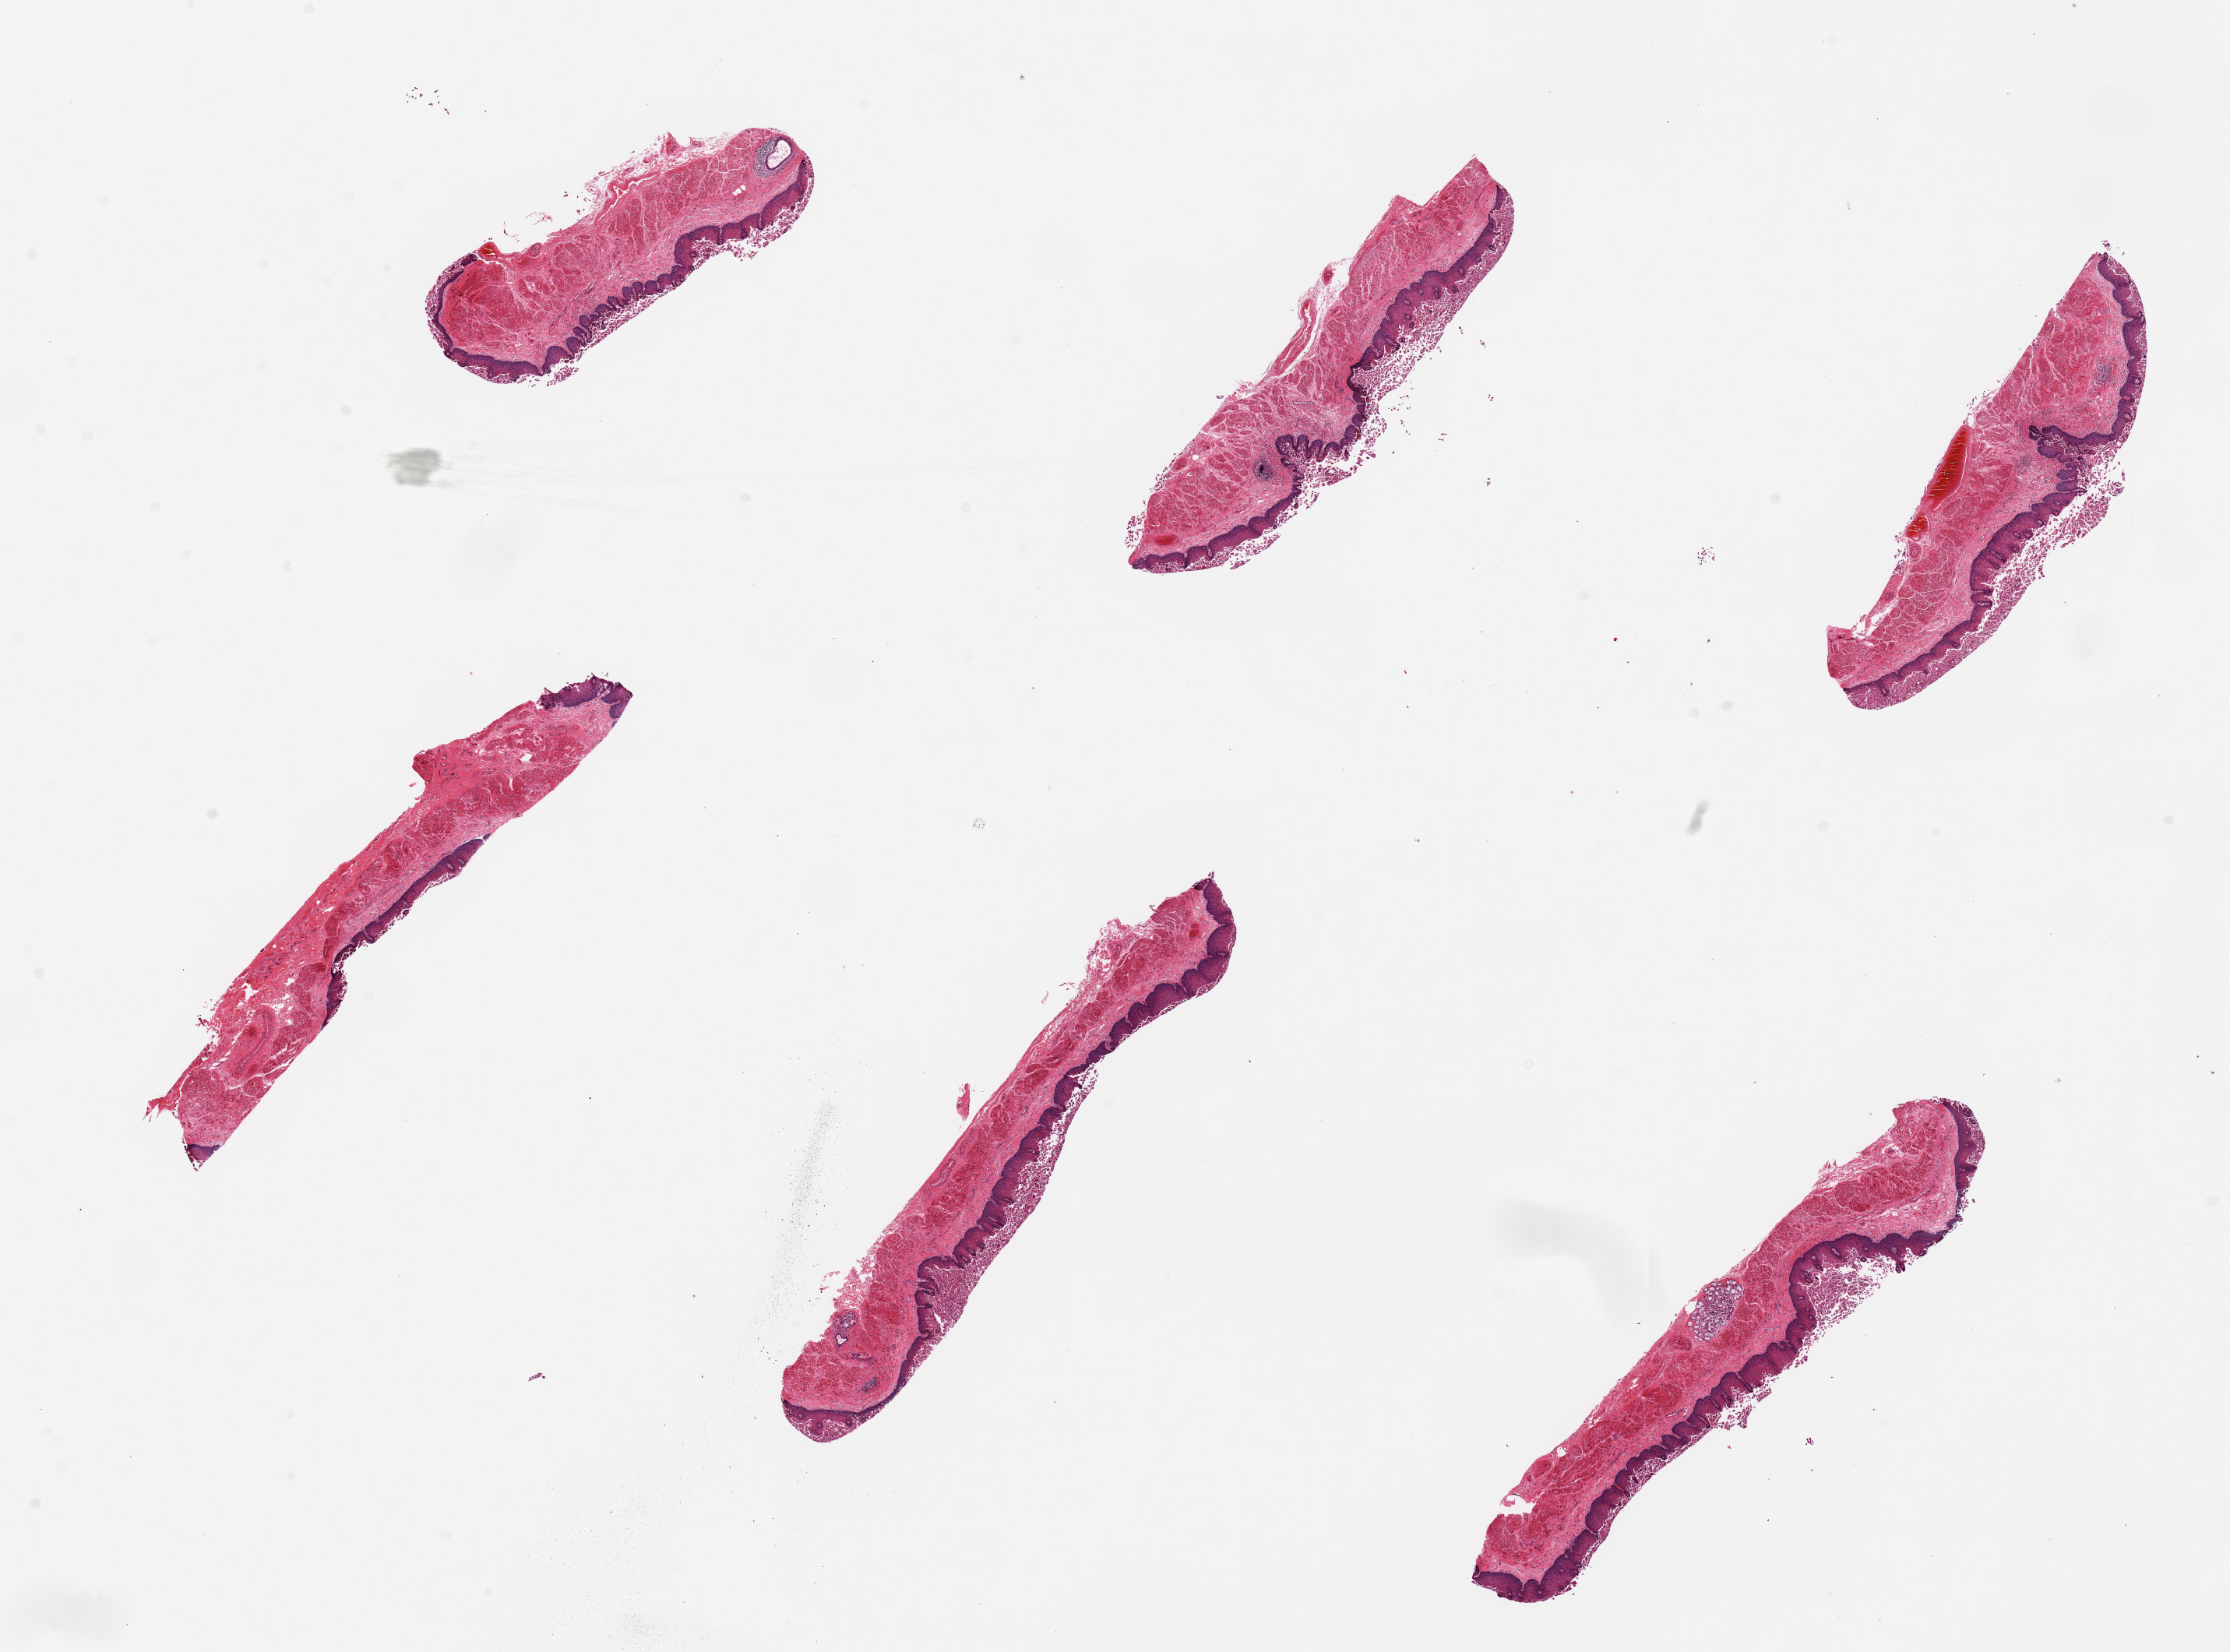
Whole-slide image, hematoxylin and eosin (H&E) stain, brightfield, shown as a low-resolution overview of the whole scanned area (about 22.6 x 16.8 mm), PAXgene-fixed, paraffin-embedded tissue, sampled site (target tissue): esophageal mucous membrane, donor tissue sample. Male donor.
Reviewer comment on this tissue sample: 6 pieces, epithelium sloughing.